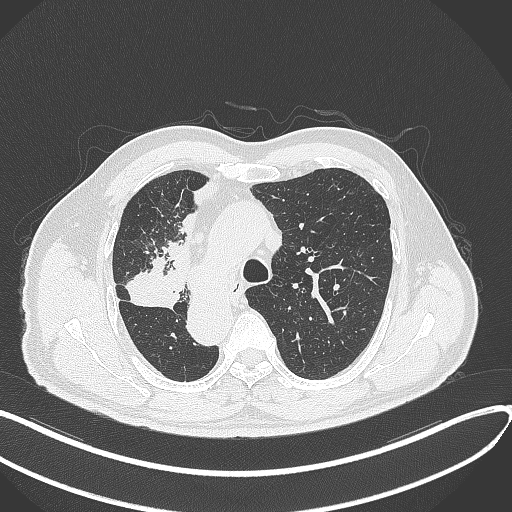
Chest CT, one axial slice; lung window (W 1500 / L -600 HU); 1 mm slice thickness; 512 × 512 image matrix, field of view 400 × 400 mm. Patient: male, 67 years. From the clinical record (not read from this slice): clinical TNM (as recorded): T2a N0 M0.
Structures marked on this image (bounding box drawn by a radiologist):
- lung tumour (recorded histology: squamous cell carcinoma): bounding box <123,252,187,311> (left, top, right, bottom; pixels)